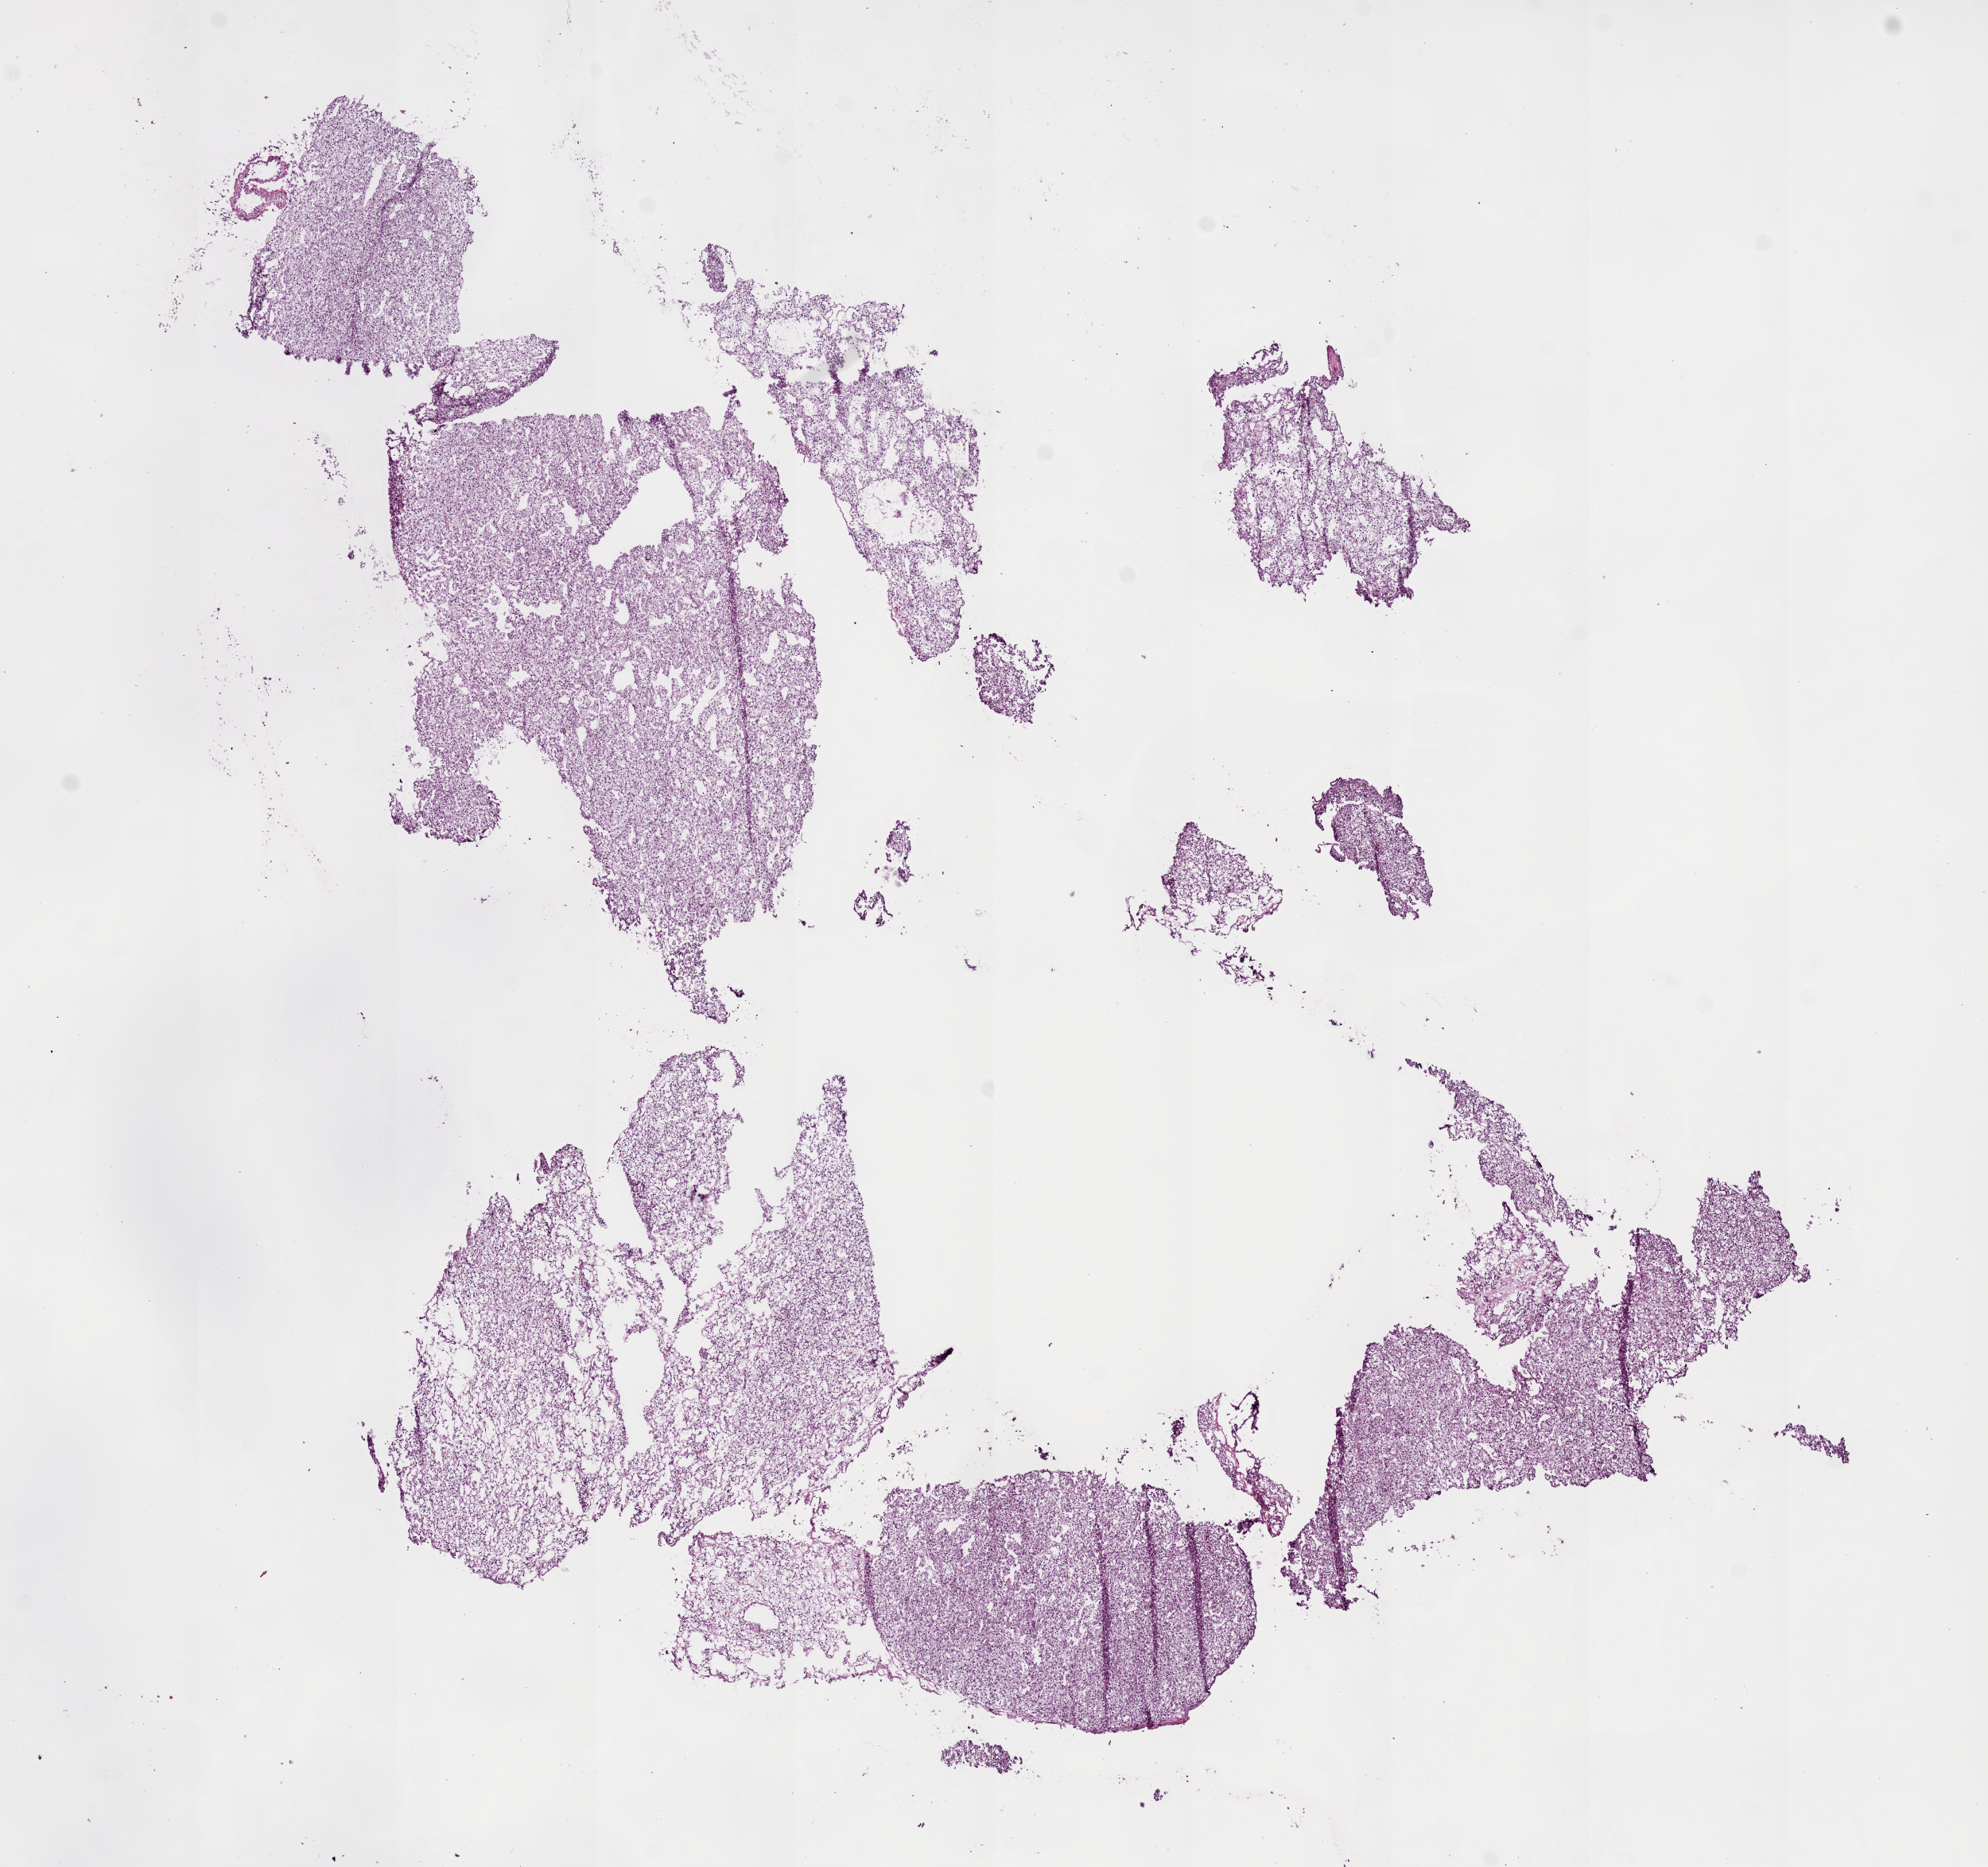
H&E whole-slide image — whole scanned area (about 10.0 x 9.4 mm) shown as a low-resolution overview; frozen section from the bottom of the tissue portion; primary tumour sample from the kidney. Female patient; age at initial diagnosis 67 years. Histologic grade: G2 (moderately differentiated). Composition of this section per pathologist review: tumour cells 95%, tumour nuclei 85%, normal cells 0%, stromal cells 5%, necrosis 0%.
AJCC pathologic stage: I. Pathologic diagnosis: Clear cell adenocarcinoma, NOS.